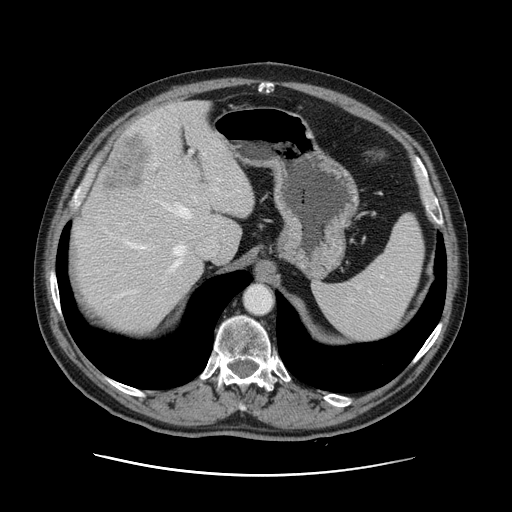
Contrast-enhanced abdominal CT, one axial slice; slice 94 of 141 in the series (ordered by position); 120 kVp; intravenous contrast given; soft-tissue window (W 400 / L 40 HU); 512 × 512 image matrix. Male patient, age 72 years. Case-level facts recorded for this patient, not image findings: diagnosis: colorectal cancer liver metastases, imaged before liver resection; multiple liver metastases: yes; largest metastasis: 5.4 cm; disease in both lobes: yes.
Structures marked on this image (expert manual segmentation):
- hepatic veins: box from (x=122, y=153) to (x=205, y=296) px
- liver: (x=70, y=102)–(x=254, y=332)
- planned liver remnant (the part of the liver to remain after resection): (x=71, y=102)–(x=255, y=332)
- portal vein (with intrahepatic branches): (x=123, y=151)–(x=218, y=253)
- liver metastasis: (x=100, y=131)–(x=151, y=195)